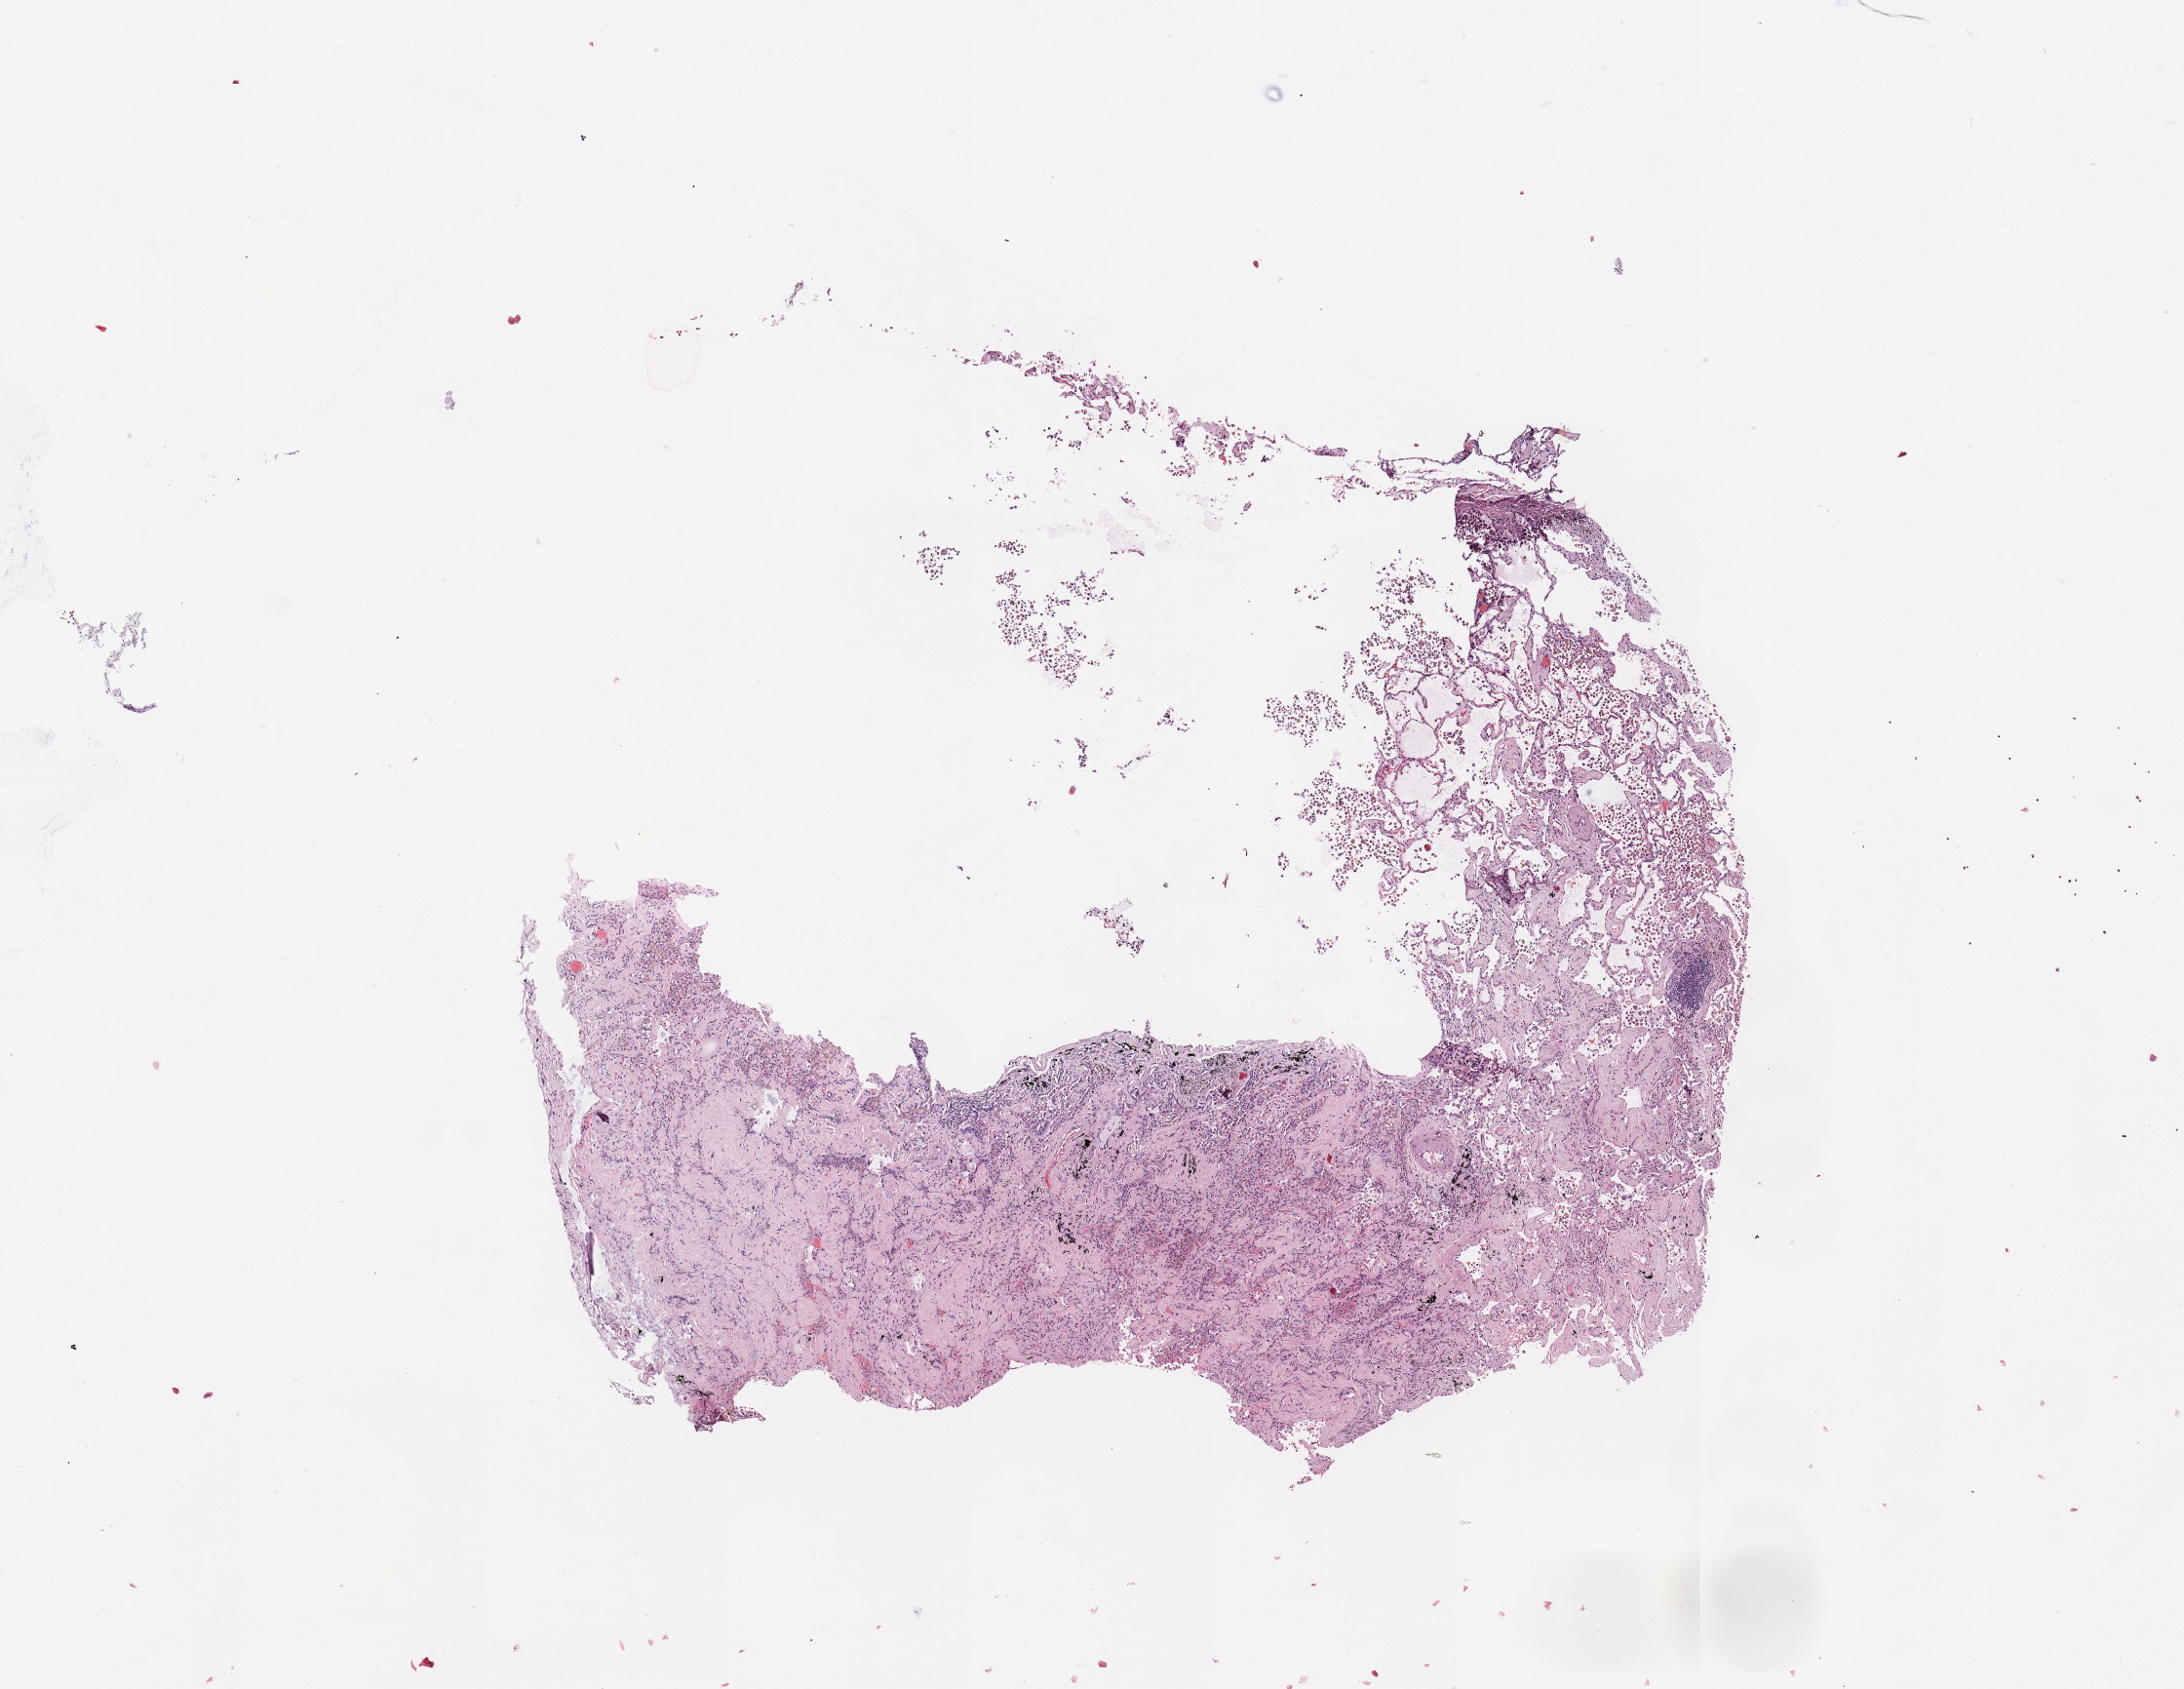
H&E-stained whole-slide image, low-resolution overview of the scanned area, about 8.9 x 6.9 mm (slide scanned at 20x), lung, normal (non-tumour) tissue. 53-year-old male patient.
This section: normal (non-tumour) tissue from the same patient. Patient diagnosis: Squamous cell carcinoma, NOS.